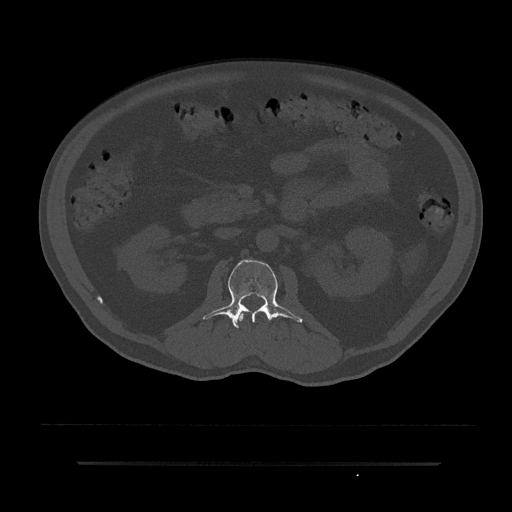
CT including the spine, one axial slice; slice 84 of 797 in the series (ordered by position); 120 kVp; bone window (W 1800 / L 400 HU); 0.5 mm slice thickness; 512 × 512 image matrix, field of view 464 × 464 mm. Patient: male, 59 years. From the clinical record (not read from this slice): primary cancer: bile ducts.
Structures marked on this image (semi-automatic segmentation, software-assisted and operator-edited):
- L1 vertebra: bounding box <236,311,247,326> (left, top, right, bottom; pixels)
- L2 vertebra: <203,260,303,328>